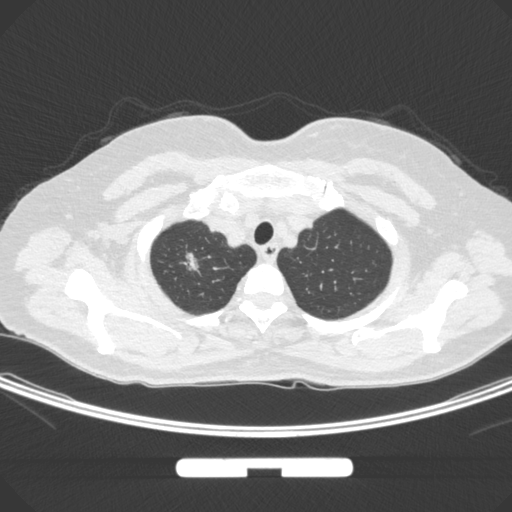
Chest CT, one axial slice; position 258 of 295 along the scan axis; 120 kVp; lung window (W 1500 / L -600 HU); 1 mm slice thickness; 512 × 512 image matrix, field of view 369 × 369 mm. Patient: female, 58 years. Case-level facts recorded for this patient, not image findings: clinical TNM (as recorded): T1b N0 M0.
Annotated regions visible in this slice (rectangle marked by the reading radiologist):
- lung tumour (recorded histology: adenocarcinoma): bounding box <178,247,210,286> (left, top, right, bottom; pixels)